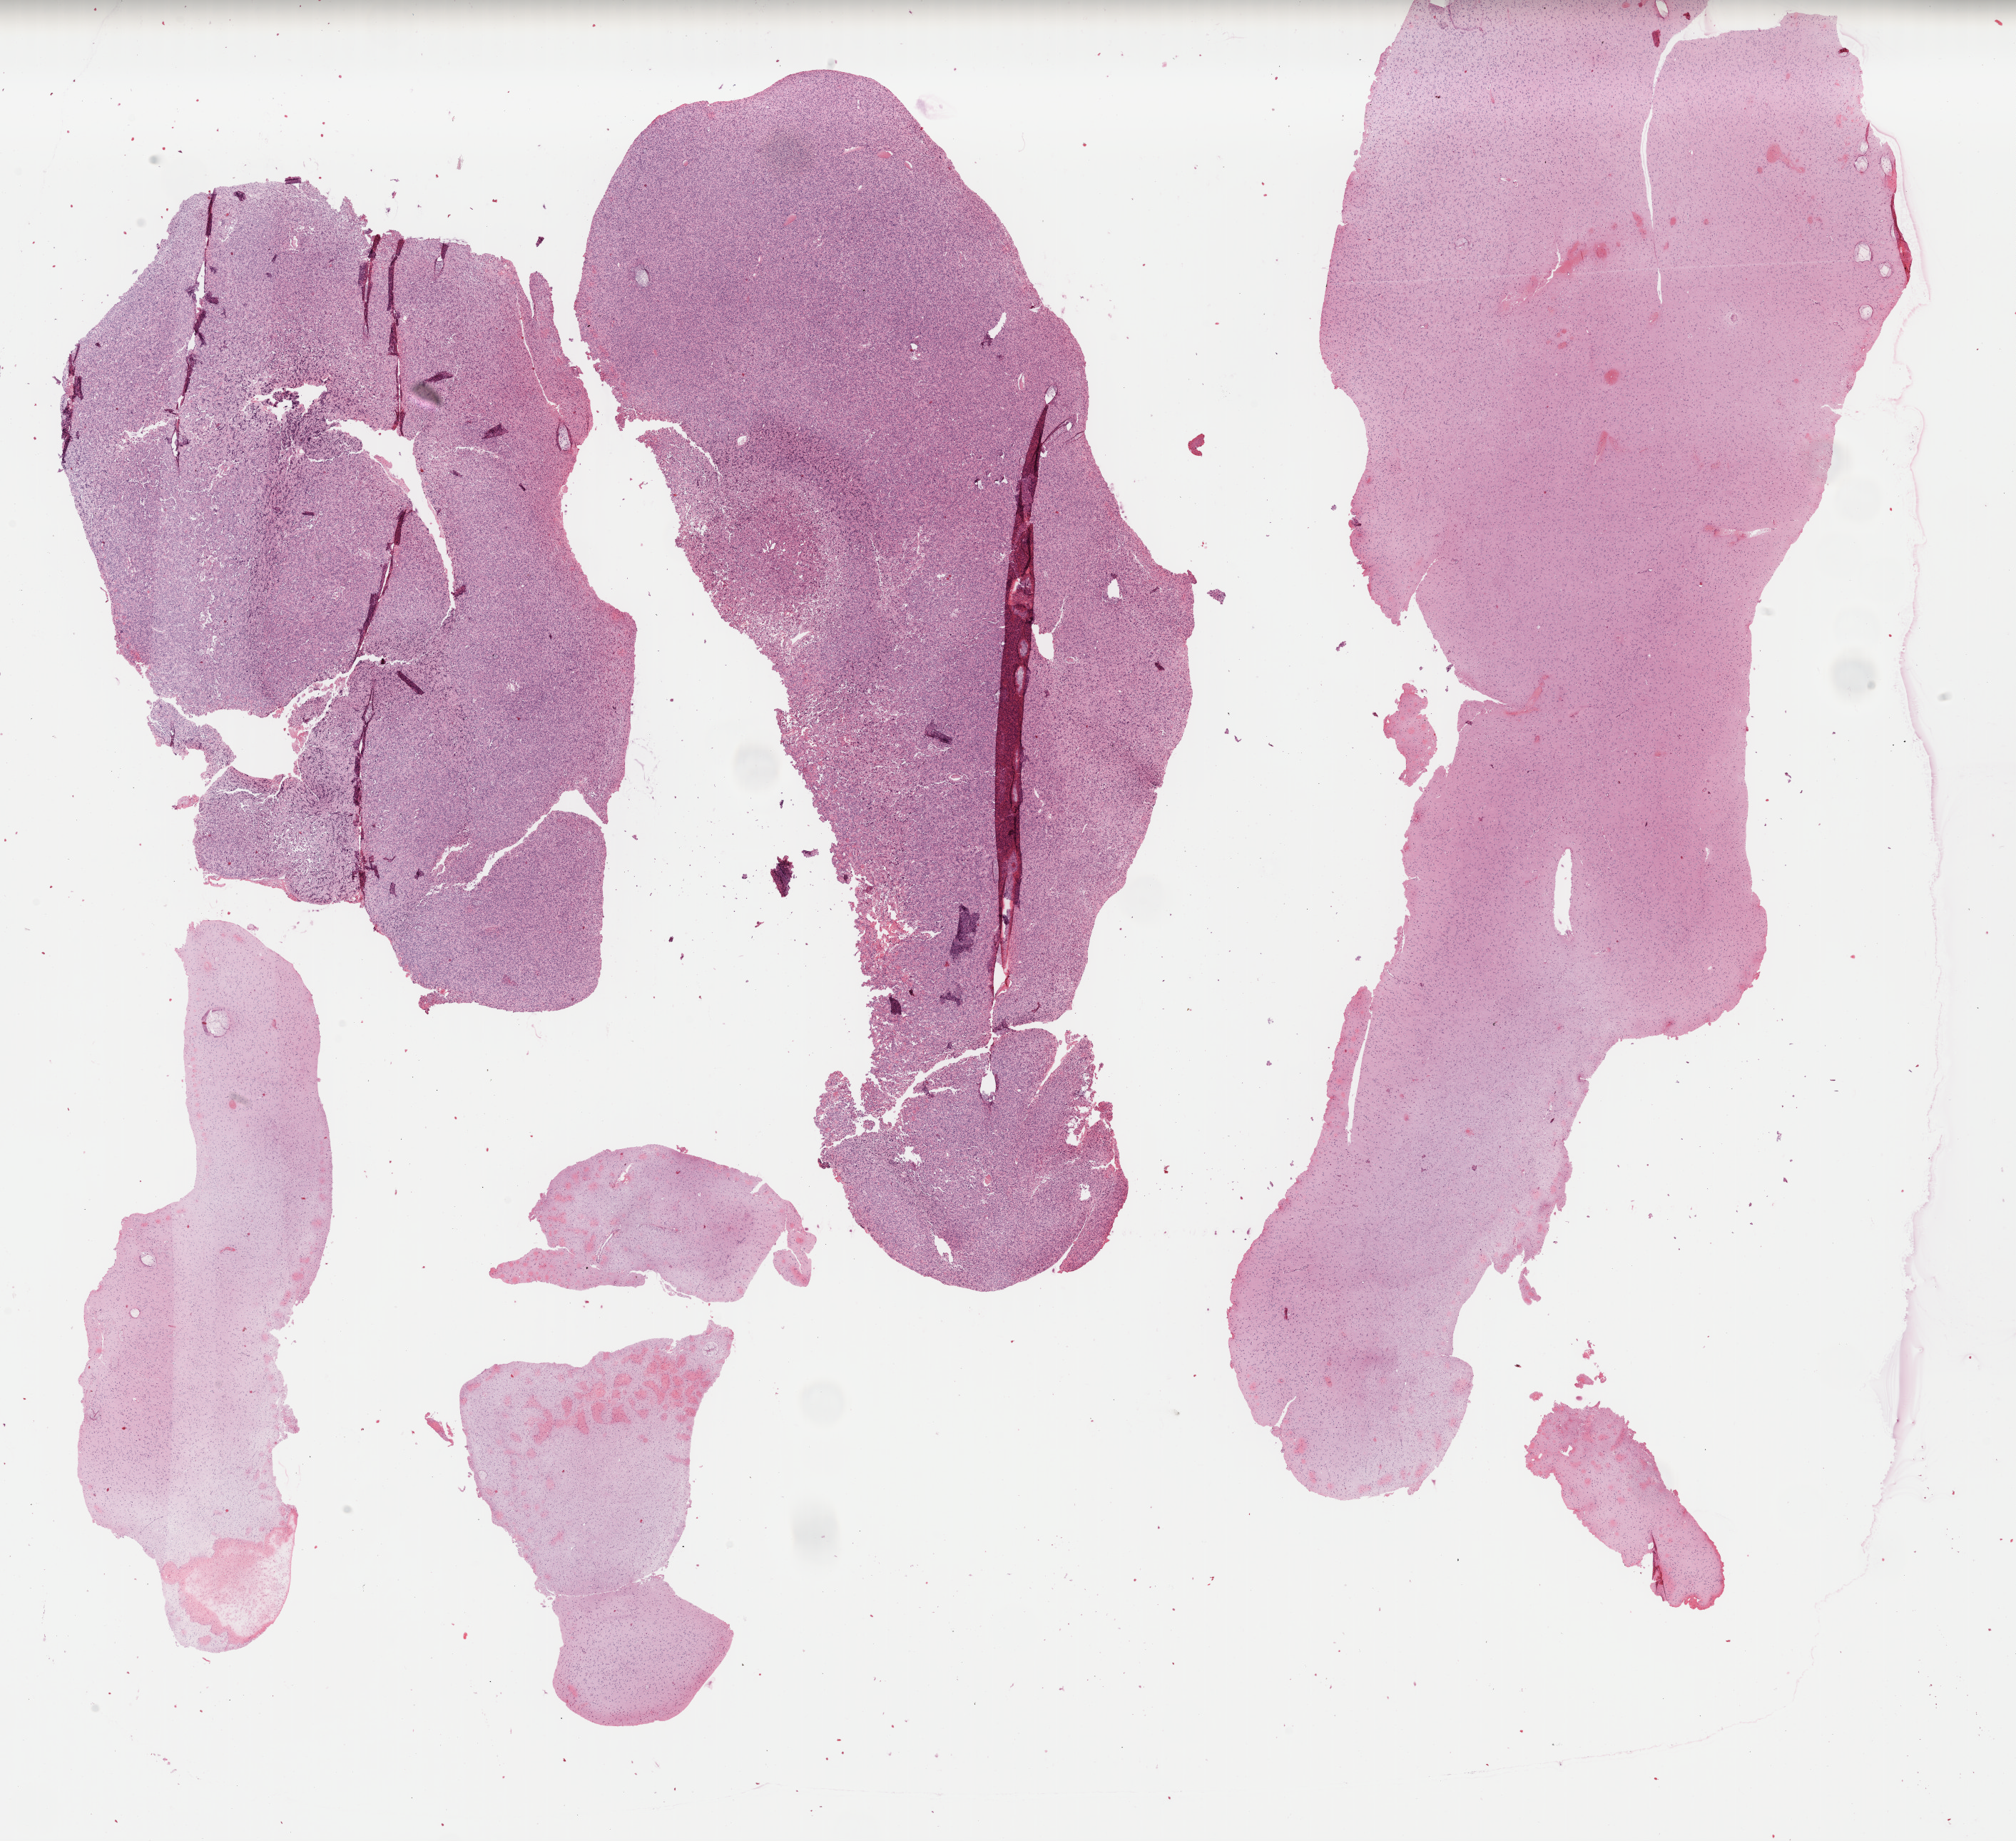
H&E-stained whole-slide image, whole scanned area (about 22.3 x 20.4 mm, slide scanned at 40x) shown as a low-resolution overview; formalin-fixed paraffin-embedded (FFPE) diagnostic section; primary tumour sample from the brain. Male, age 51 years at initial diagnosis. Histologic grade: G3 (poorly differentiated).
* pathologic diagnosis: Mixed glioma (cerebrum)